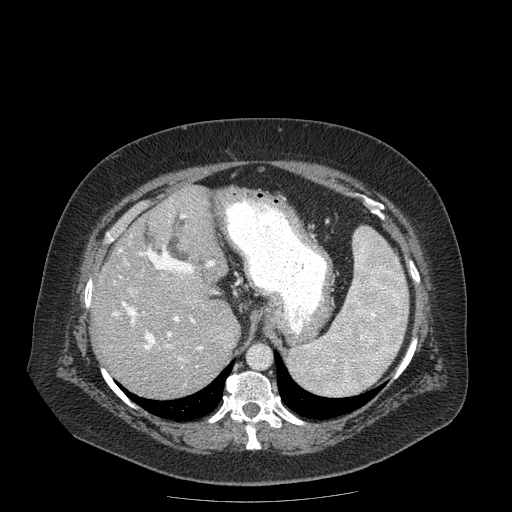
Contrast-enhanced abdominal CT (liver protocol), one axial slice. Slice 125 of 204 in the series (ordered by position). Reconstruction kernel STANDARD. 120 kVp. Soft-tissue window (W 400 / L 40 HU). 512 × 512 image matrix, field of view 440 × 440 mm. Case-level facts recorded for this patient, not image findings: diagnosis: hepatocellular carcinoma (patient treated with transarterial chemoembolisation; whether this scan precedes or follows treatment is not stated here); TNM stage (as recorded): Stage-IIIB; Child-Pugh class: A; tumour differentiation: well differentiated; tumour nodularity: uninodular.
Outlined on this slice (semi-automatically segmented with operator editing):
- abdominal aorta: bounding box <249,345,271,367> (left, top, right, bottom; pixels)
- liver parenchyma outside the tumour (the mass and vessels are separate outlines, so this box may not span the whole liver): <92,186,238,398>
- liver vessels: <112,214,215,367>